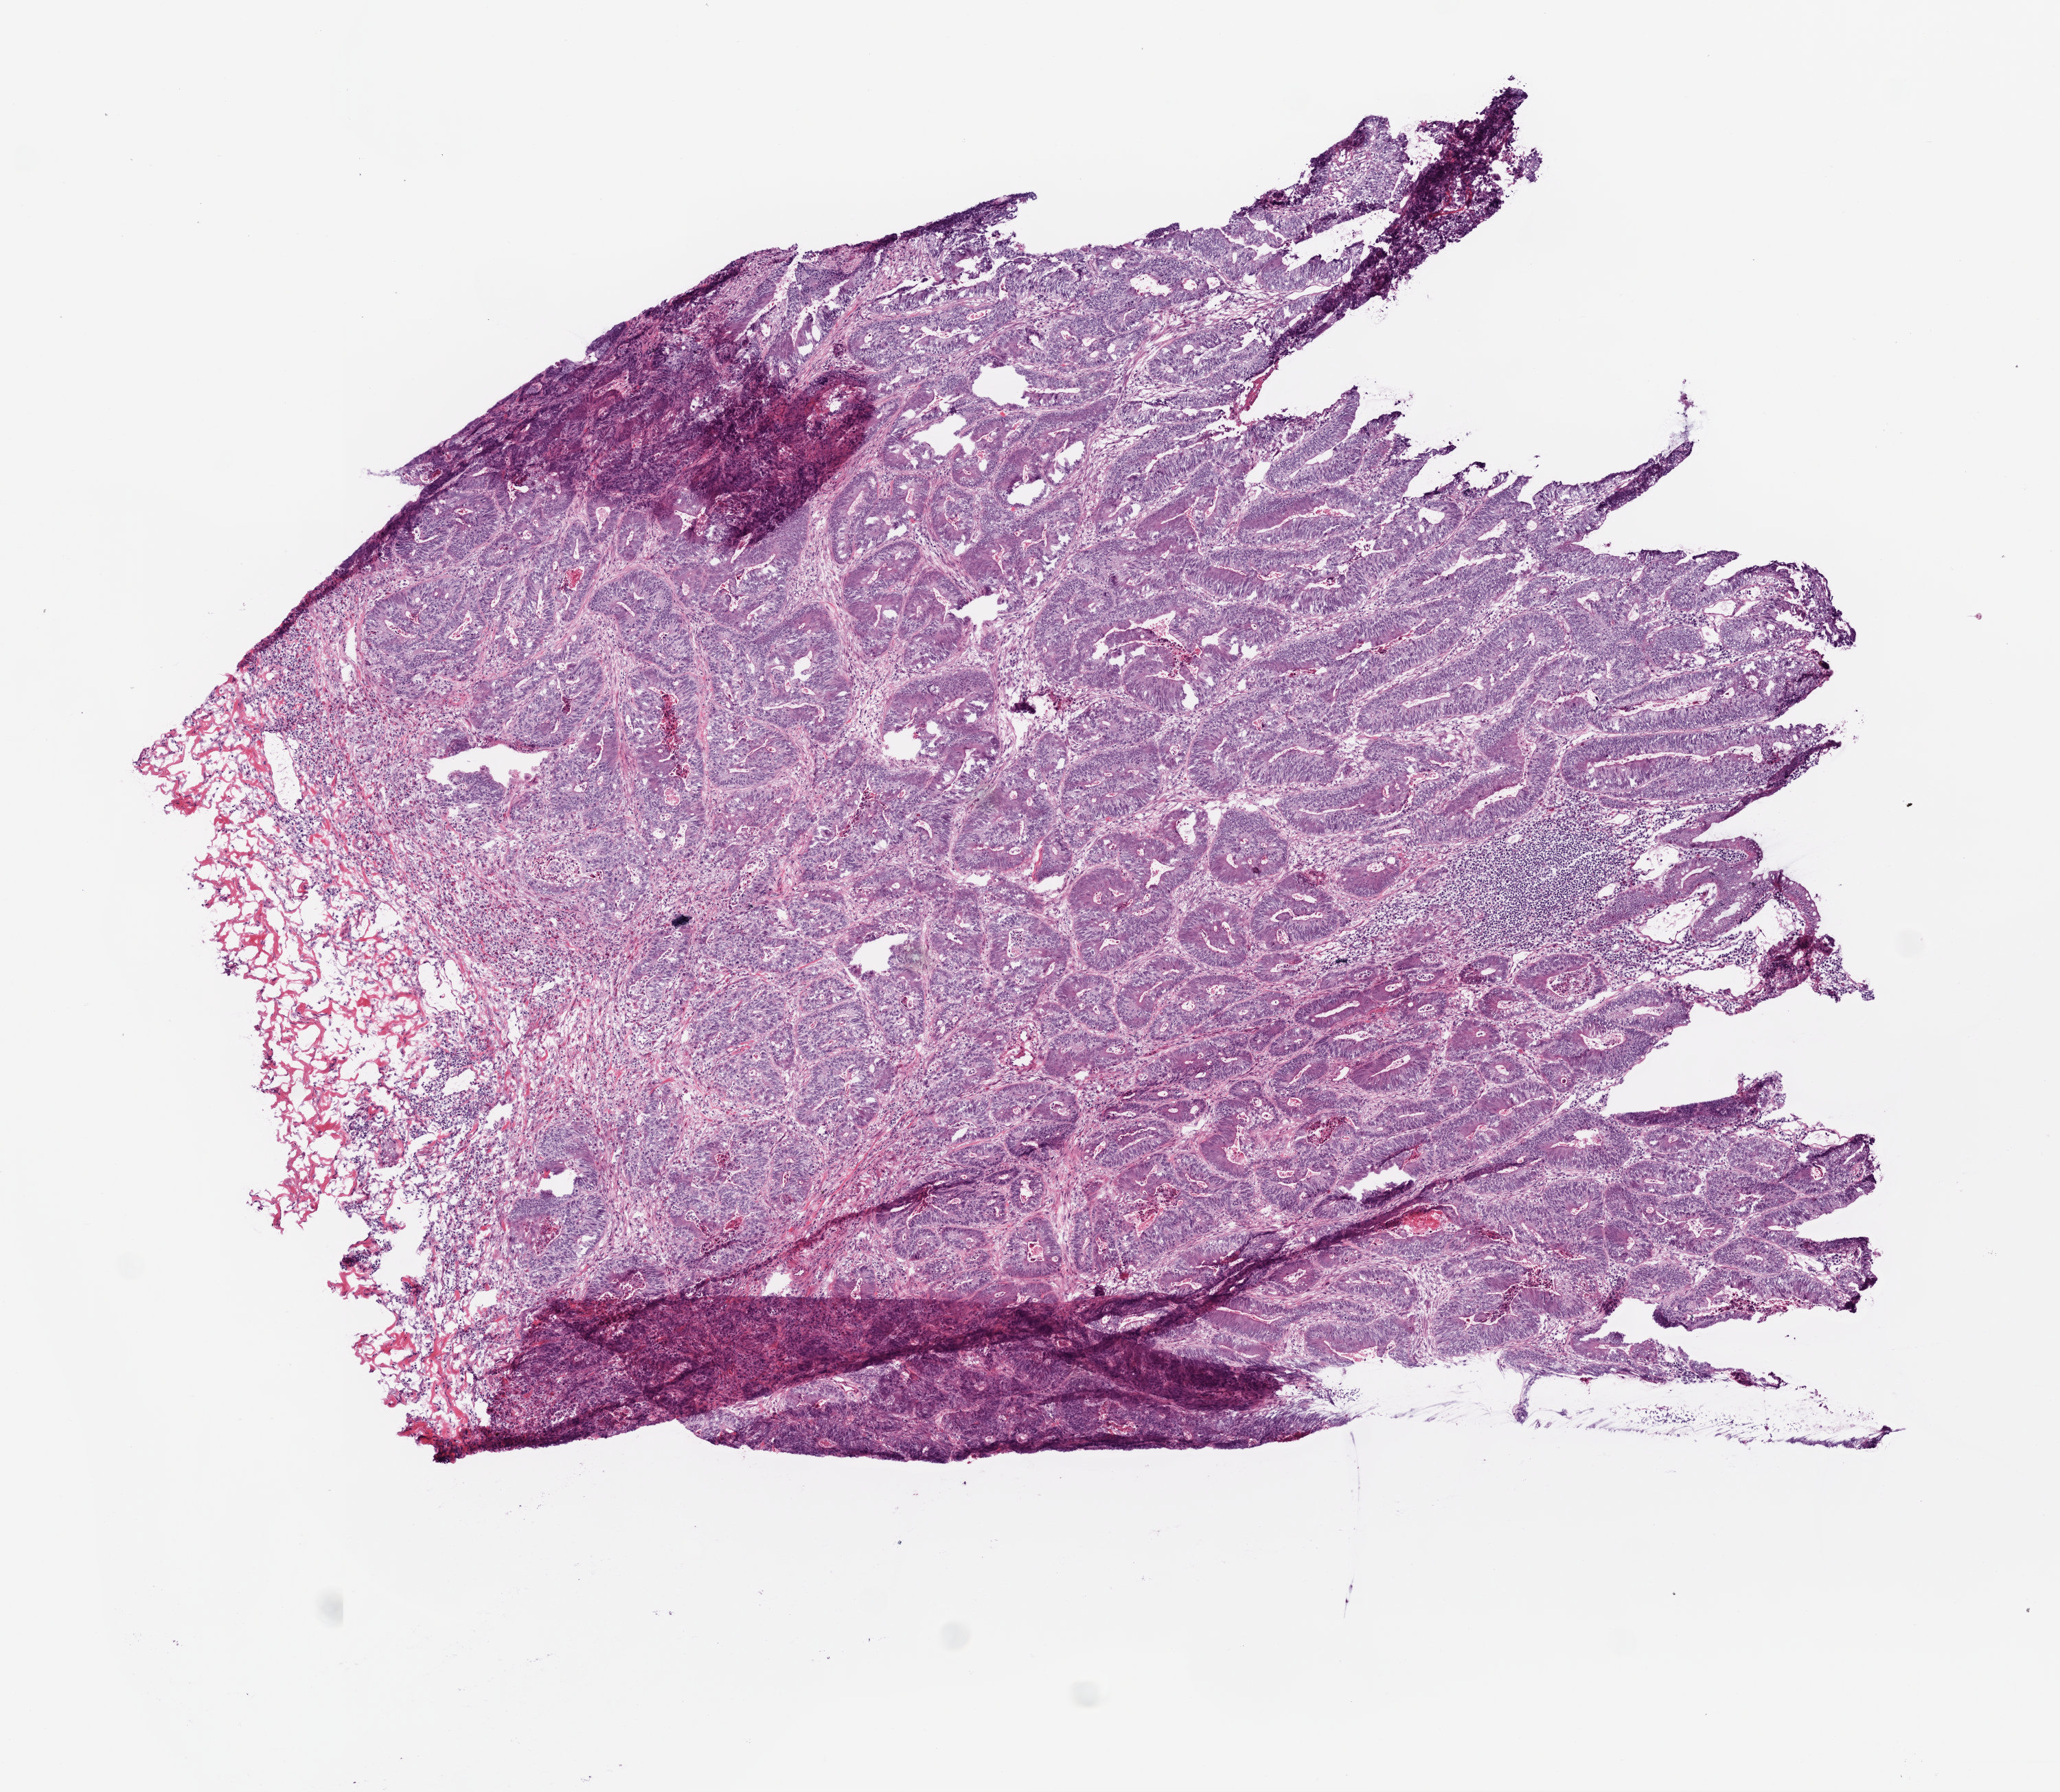
Whole-slide histology image, H&E, shown as a low-resolution overview of the whole scanned area (about 6.0 x 5.2 mm, from a 20x scan). Frozen section. Primary tumour sample from the colon. Patient: male, age at initial diagnosis 85 years. Slide review estimates, as recorded: tumour cells 80%, tumour nuclei 90%.
Diagnosis: Adenocarcinoma, NOS (sigmoid colon).